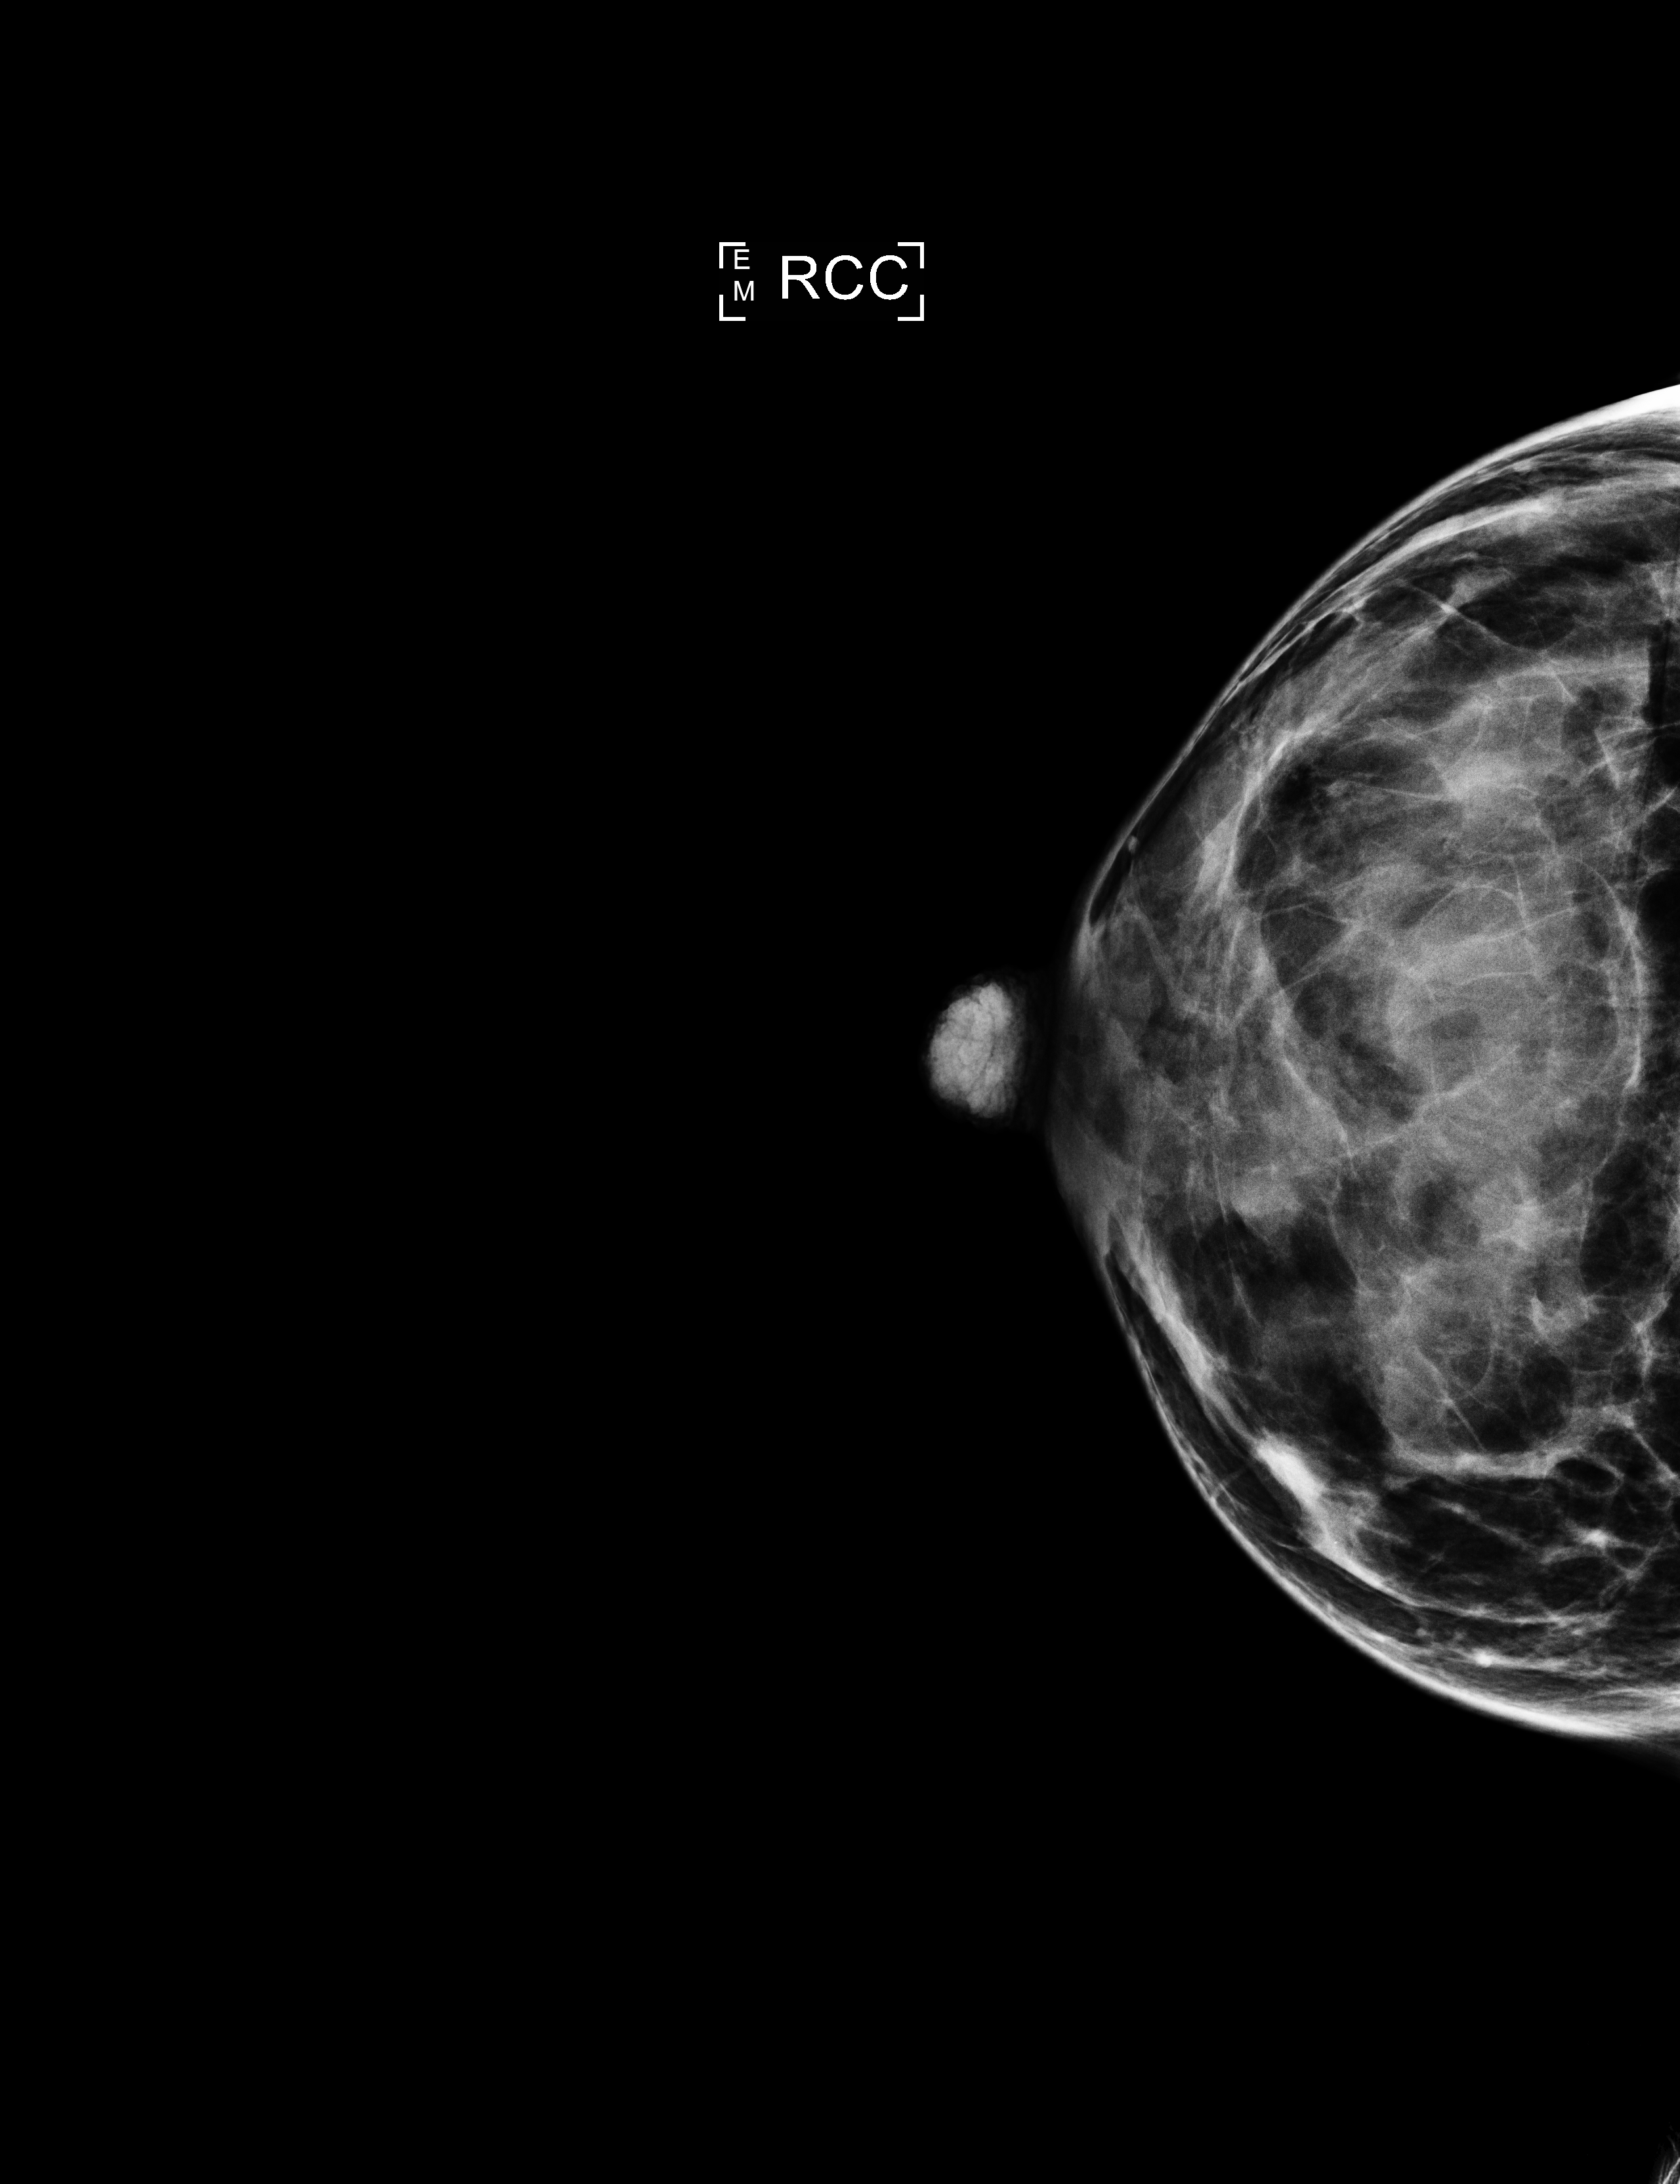
Digital mammogram (FFDM); right breast; cranio-caudal projection; screening examination. Patient aged 42 years (female).
BI-RADS breast density category at the screening exam (both breasts, scale 1–4): 4. Final BI-RADS category for the screening round (tomosynthesis exam, both breasts): category 2. Recall: recalled for additional imaging after this screen.